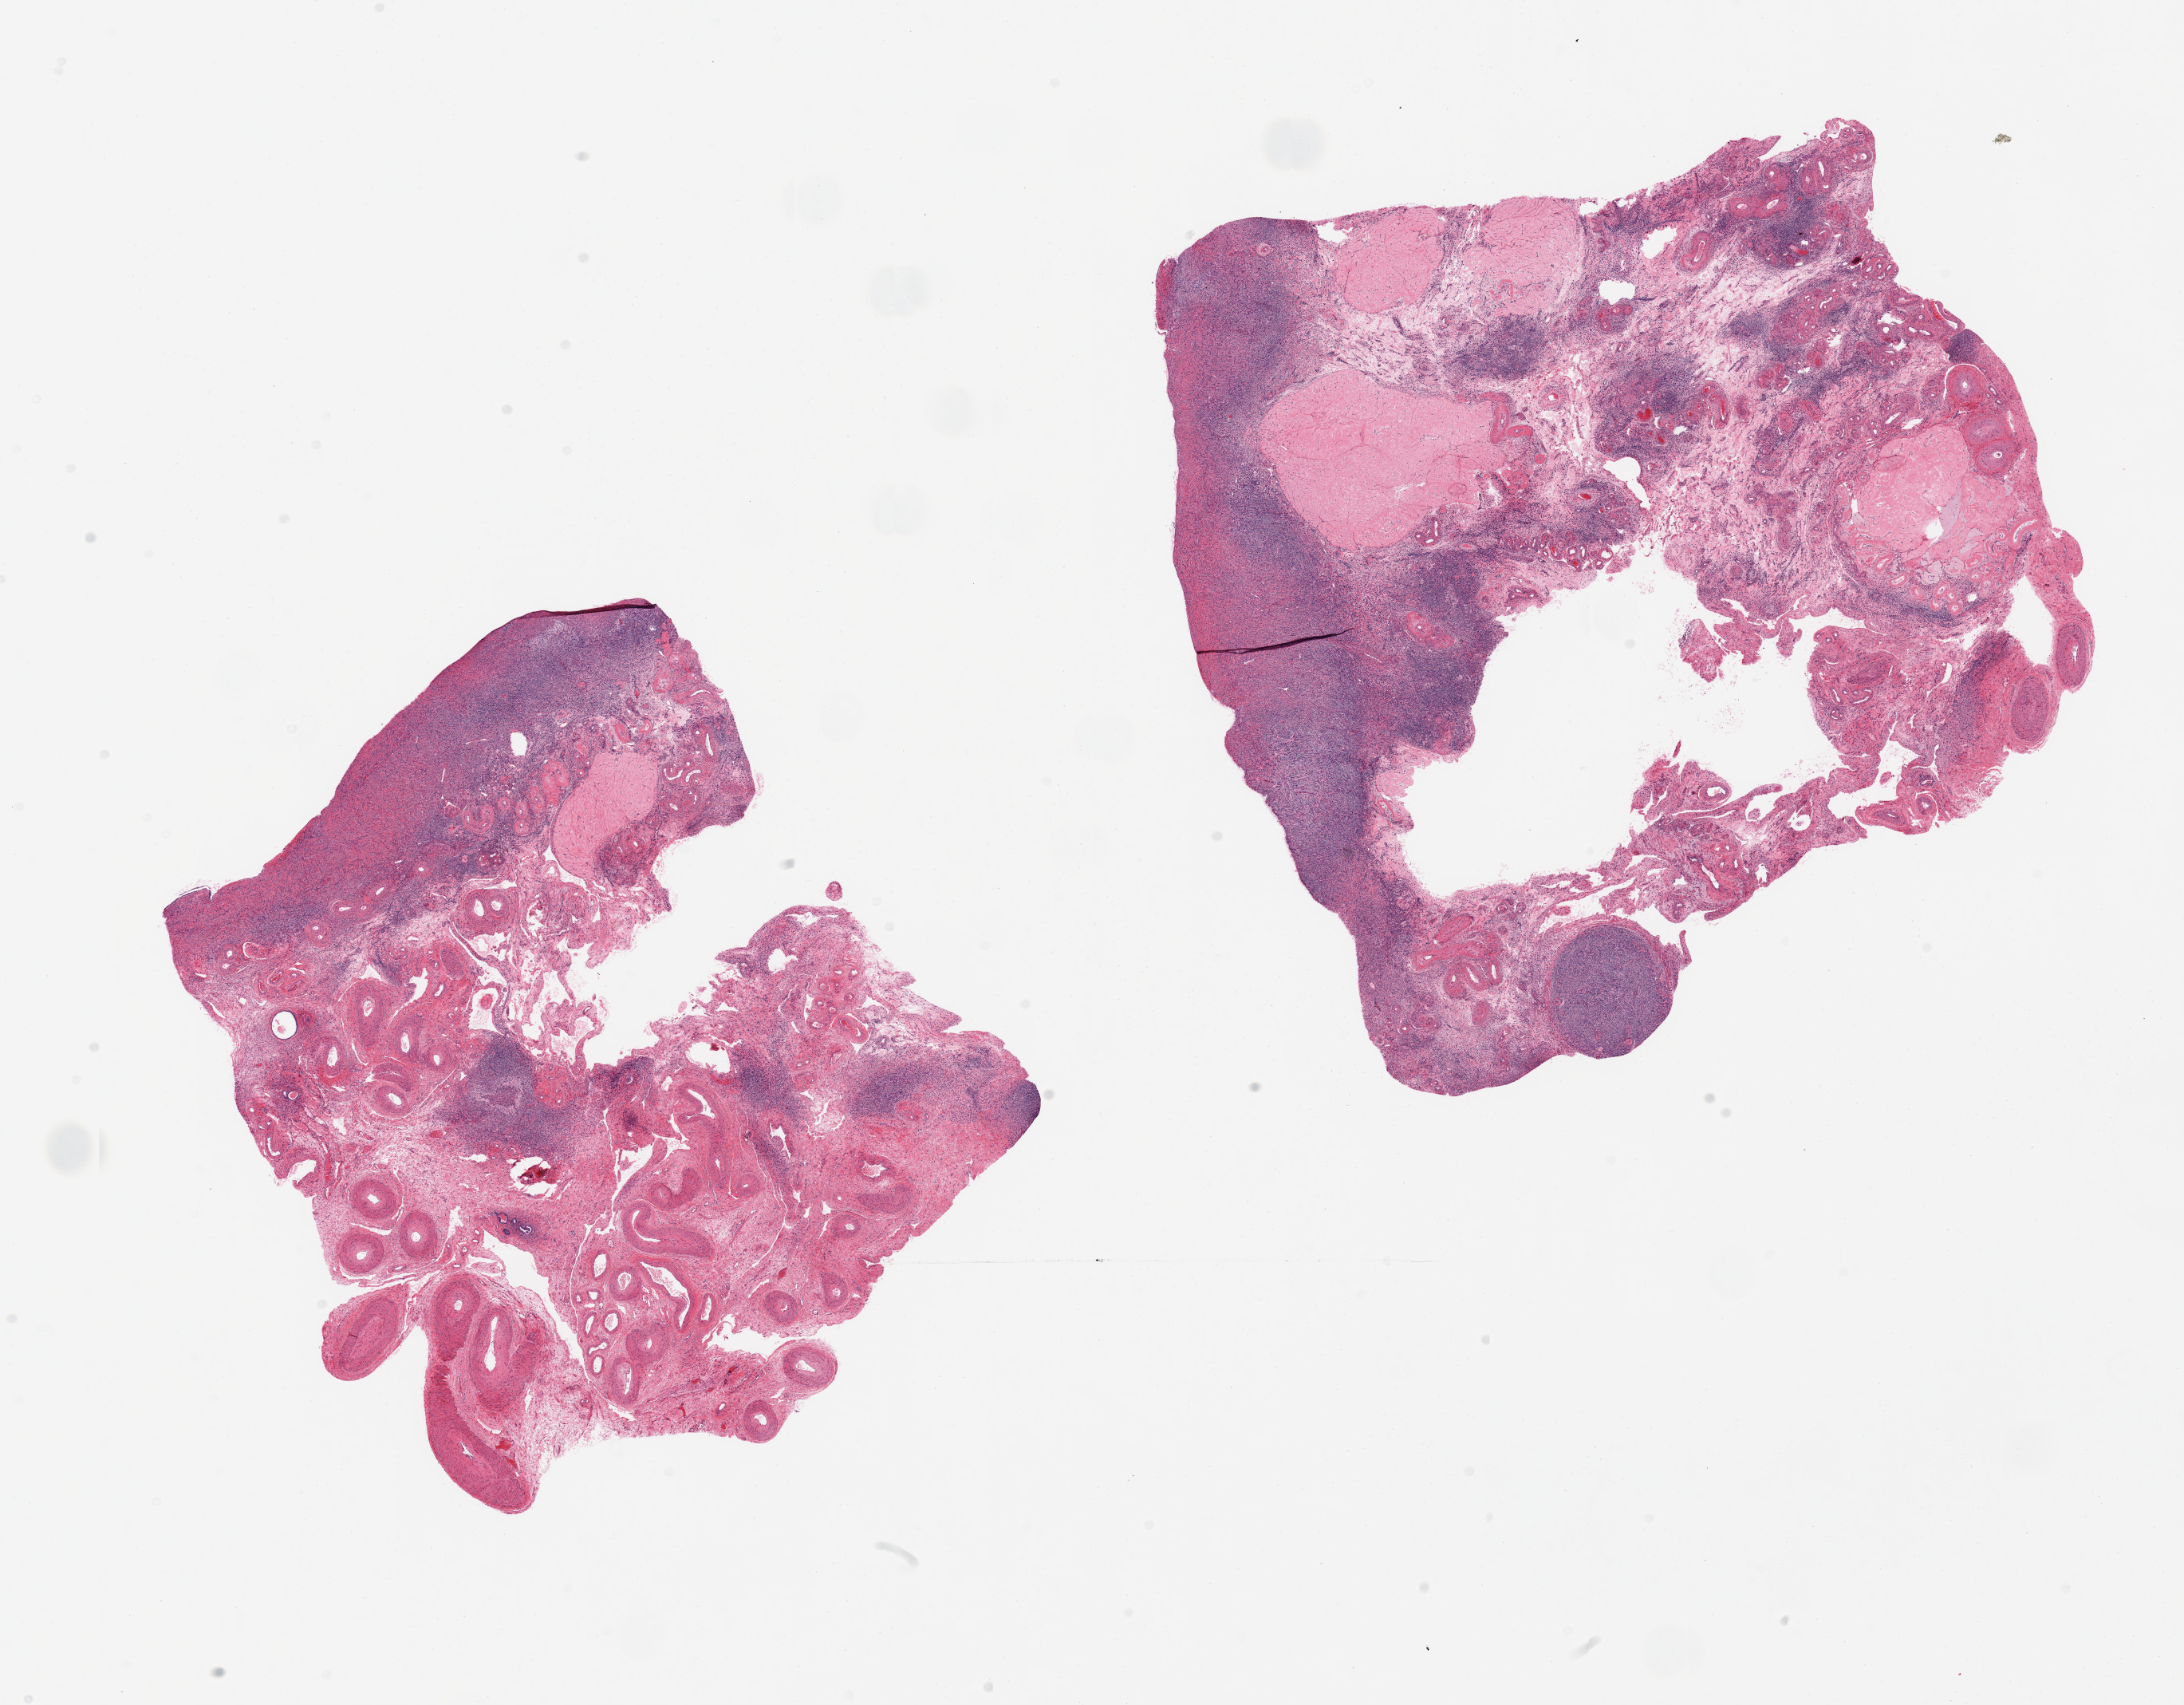
Hematoxylin and eosin (H&E) whole-slide image — shown as a low-resolution overview of the whole scanned area (about 21.7 x 16.9 mm, from a 20x scan); PAXgene-fixed paraffin-embedded (PFPE) section; sampled site (target tissue): ovary; tissue donor sample. Donor: female.
Reviewer comment on this tissue sample: 2 pieces, several corpora albicantia, hilus with numerous vessels, rete ovarii.